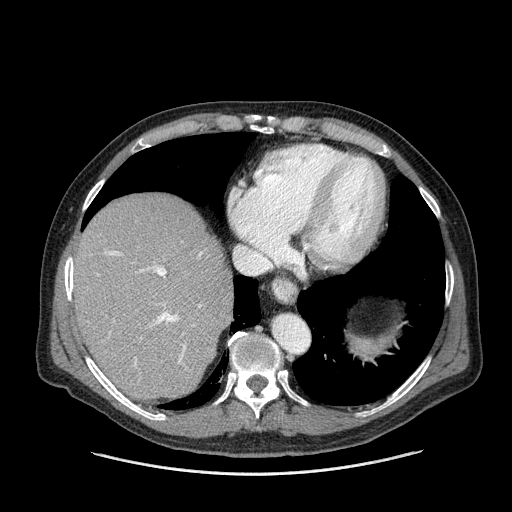
Contrast-enhanced abdominal CT (liver protocol), one axial slice. Slice 124 of 180 in the series (ordered by position). One of 2 acquisitions stored at this slice position. Soft-tissue window (W 400 / L 40 HU). 2.5 mm slice thickness. 512 × 512 image matrix, field of view 420 × 420 mm. From the clinical record (not read from this slice): diagnosis: hepatocellular carcinoma (patient treated with transarterial chemoembolisation; whether this scan precedes or follows treatment is not stated here); TNM stage (as recorded): Stage-II; Child-Pugh class: A; tumour nodularity: multinodular.
Outlined on this slice (semi-automatically segmented with operator editing):
- abdominal aorta: bounding box [x1, y1, x2, y2] px = [273, 316, 309, 352]
- liver parenchyma outside the tumour (the mass and vessels are separate outlines, so this box may not span the whole liver): [76, 196, 232, 400]
- liver vessels: [98, 251, 203, 366]